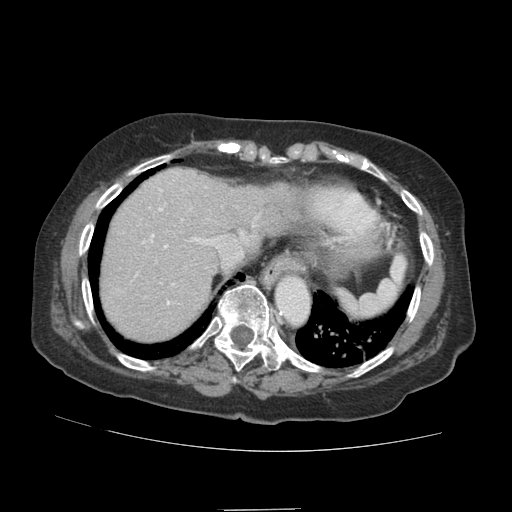
Contrast-enhanced abdominal CT (liver protocol), one axial slice. Position 74 of 89 along the scan axis. Soft-tissue window (W 400 / L 40 HU). 512 × 512 image matrix. From the clinical record (not read from this slice): diagnosis: hepatocellular carcinoma (patient treated with transarterial chemoembolisation; whether this scan precedes or follows treatment is not stated here); TNM stage (as recorded): Stage-II; Child-Pugh class: A; tumour differentiation: moderately differentiated; tumour nodularity: multinodular.
Annotated regions visible in this slice (semi-automatically segmented with operator editing):
- abdominal aorta: bounding box [x1, y1, x2, y2] px = [276, 278, 309, 322]
- liver parenchyma outside the tumour (the mass and vessels are separate outlines, so this box may not span the whole liver): [100, 168, 304, 340]
- liver vessels: [136, 188, 258, 305]